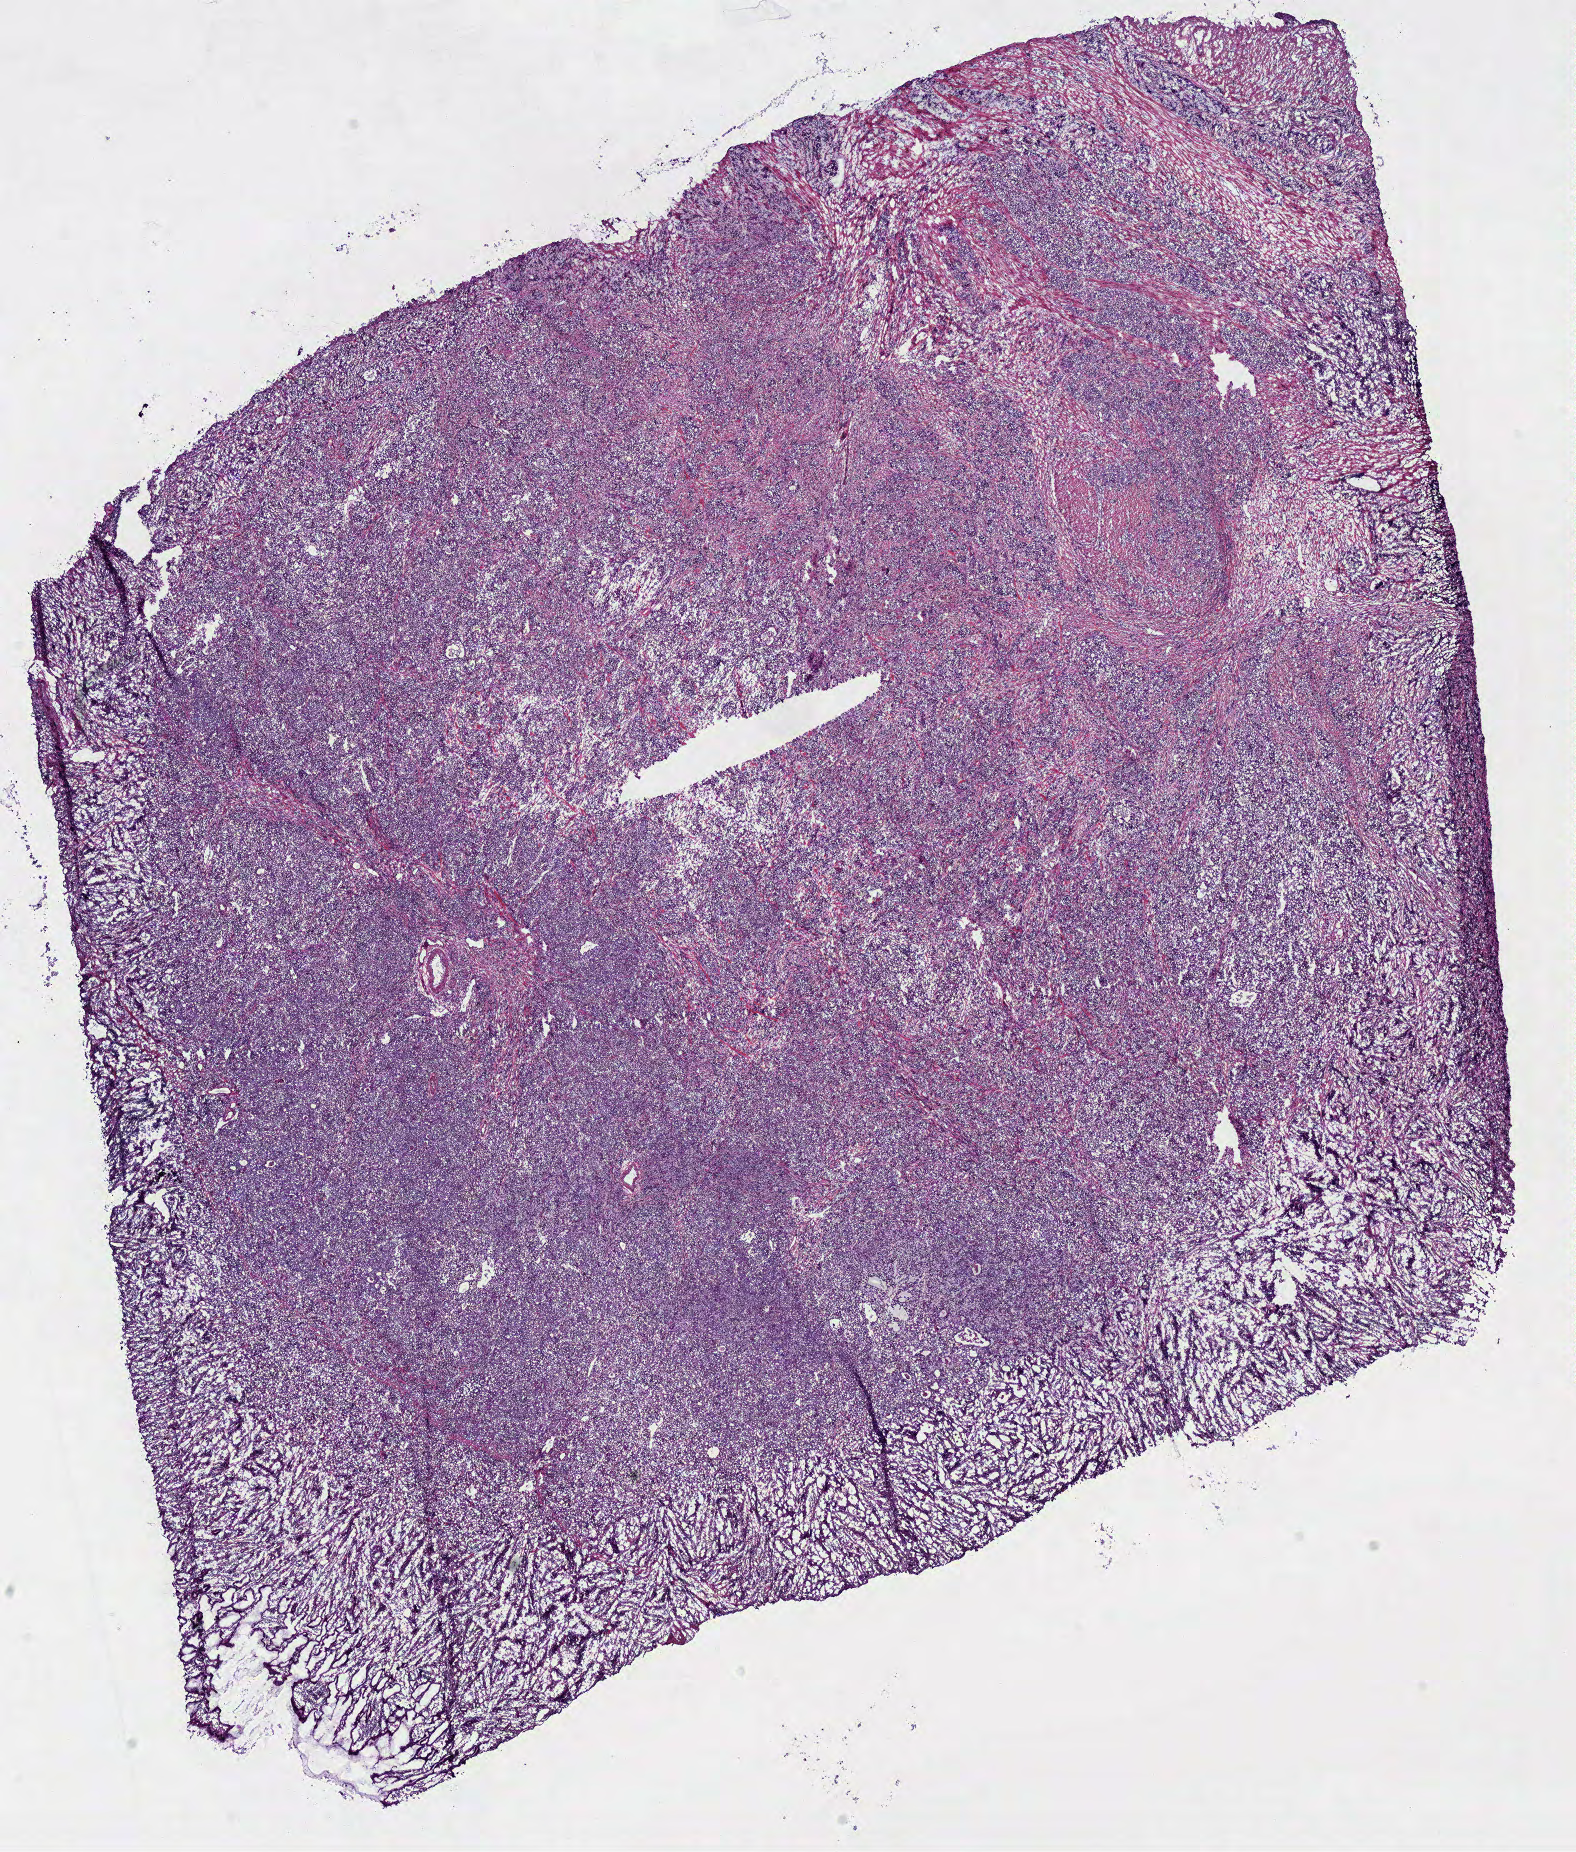
Digitized H&E tissue section (whole slide), whole scanned area (about 12.4 x 14.6 mm, slide scanned at 40x) shown as a low-resolution overview; frozen section from the bottom of the tissue portion; sample: primary tumour, stomach. Male patient; age at initial diagnosis 69 years. Histologic grade: G3 (poorly differentiated). Pathologist review of this section (percent, as recorded): tumour cells 90%, tumour nuclei 80%, normal cells 0%, stromal cells 10%, necrosis 0%.
AJCC pathologic stage: IIIA (6th edition). Diagnosis: Adenocarcinoma, NOS (gastric antrum).